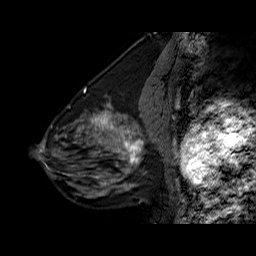
Breast MRI (dynamic contrast-enhanced), one sagittal slice; slice 25 of 60 in the series (ordered by position); dynamic contrast-enhanced series, time point 2 of 6 at this slice position (early post-contrast); 1.5 T; TE 6.3 ms, TR 32.5 ms; 4 mm slice thickness; 256 × 256 image matrix, field of view 200 × 200 mm. Female patient. From the clinical record (not read from this slice): setting: breast cancer imaged before/during neoadjuvant chemotherapy; receptor status: triple-negative.
Structures marked on this image (semi-automatically segmented with operator editing):
- analysis volume of interest (the breast-tissue region the enhancement analysis was run in; not a lesion): bounding box (x1, y1, x2, y2) in pixels: (108, 126, 154, 177)
- tumour enhancement mask (voxels above the 100 % enhancement threshold inside the analysis volume of interest): (109, 126, 143, 171)